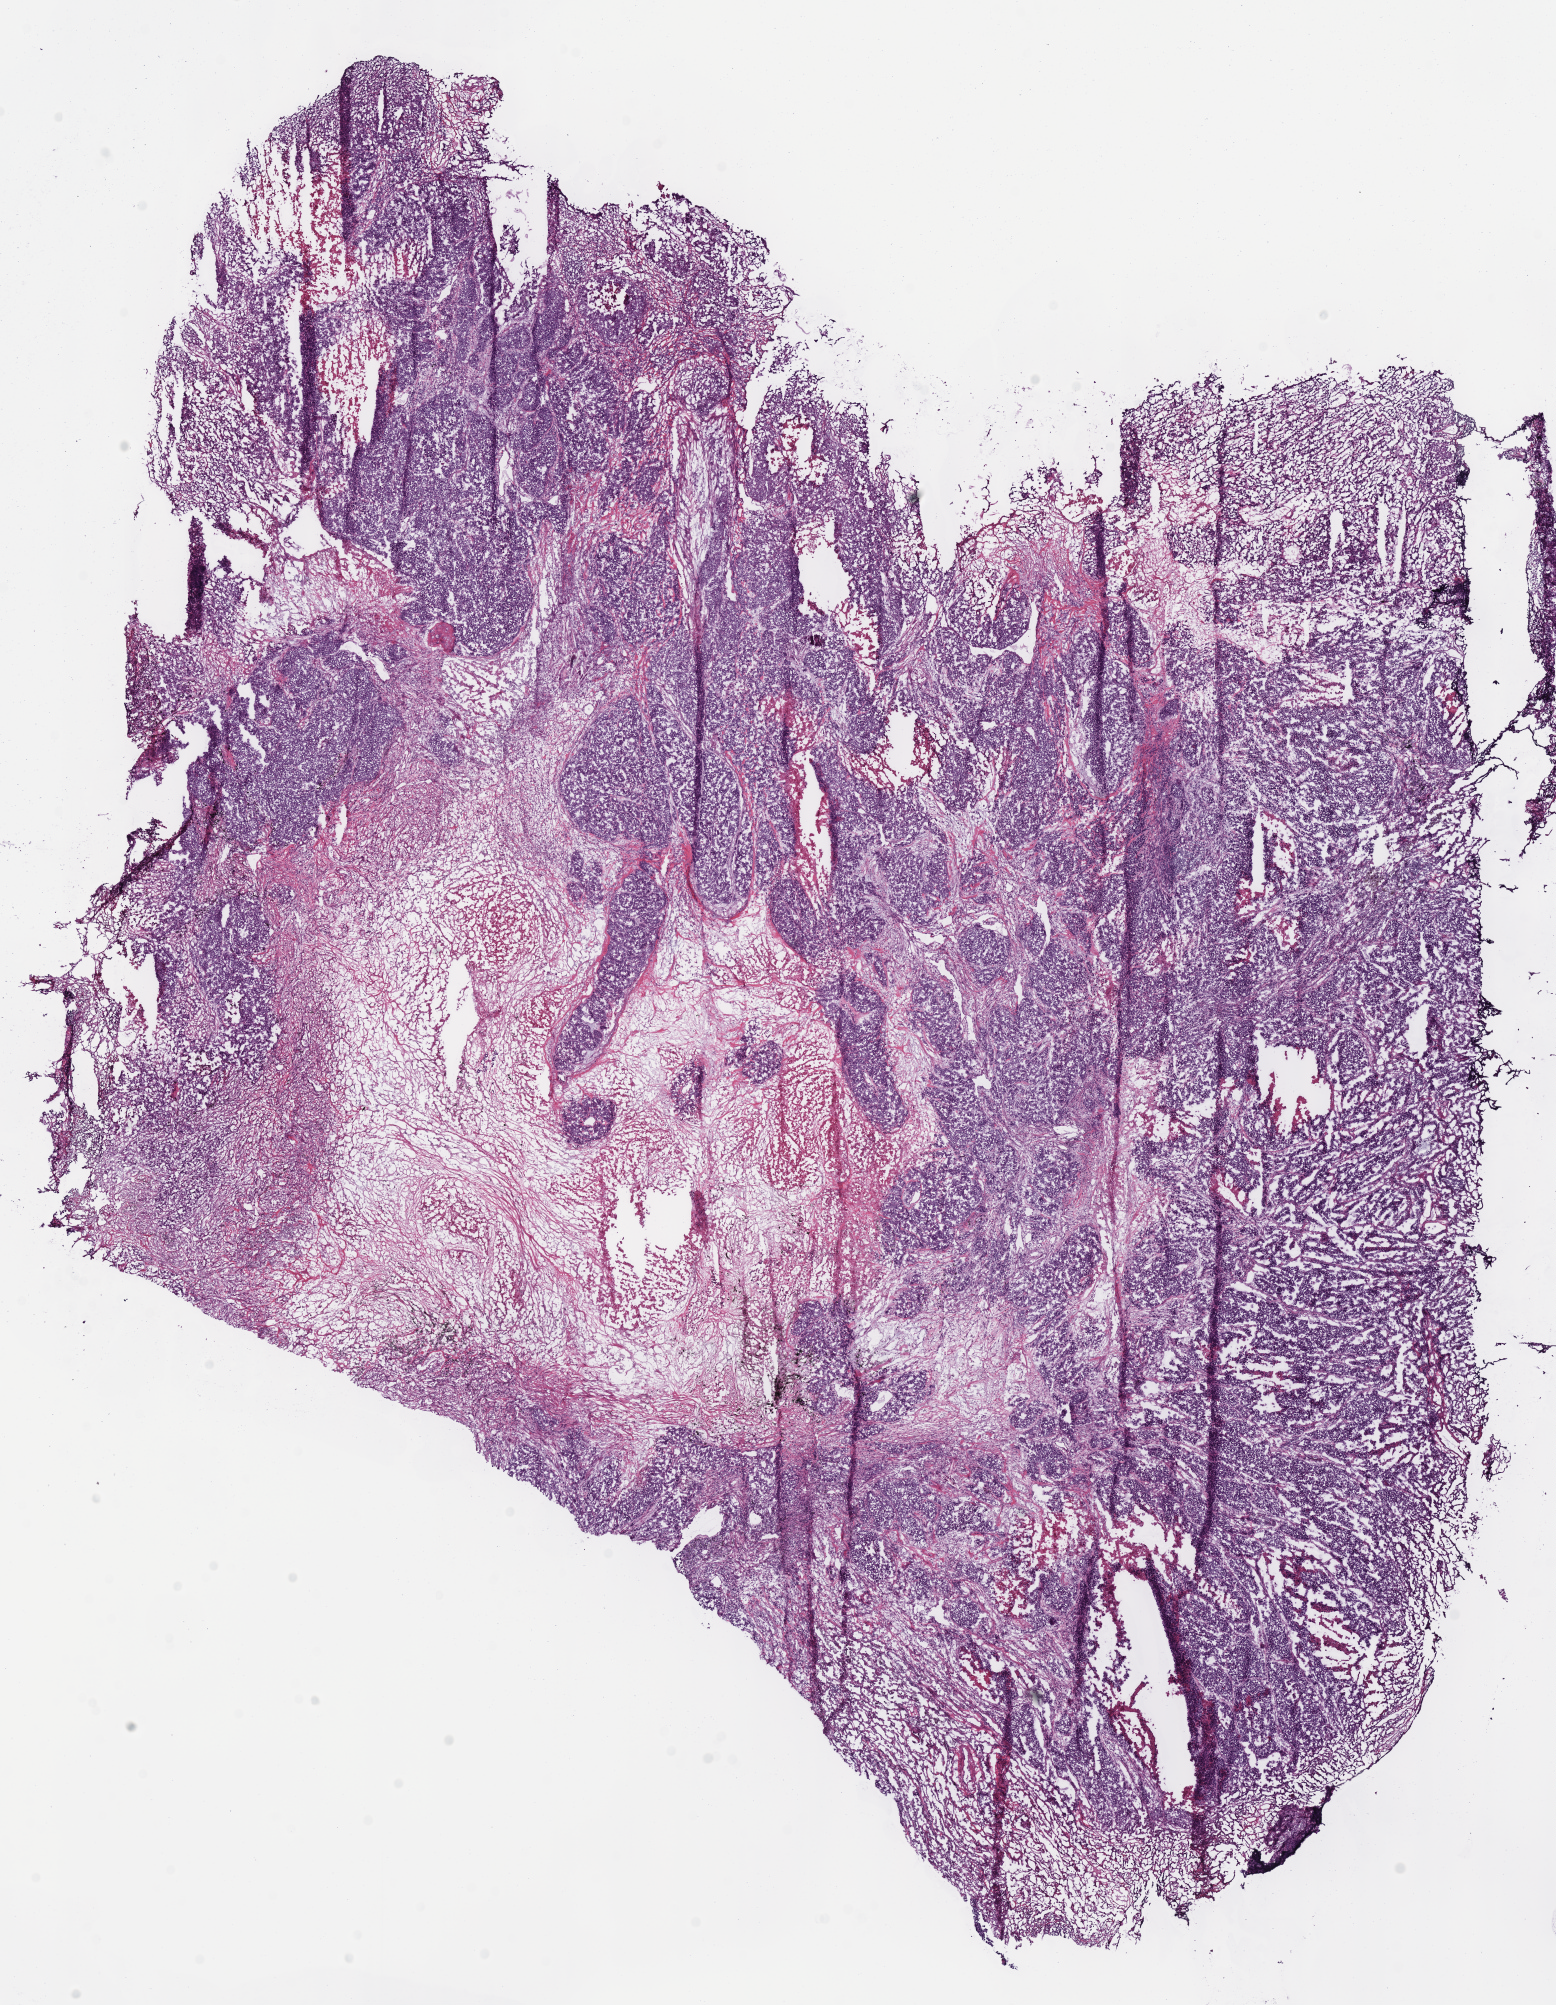
Digitized H&E tissue section (whole slide), a low-resolution overview of the entire scanned area, about 12.2 x 15.8 mm (slide scanned at 40x); frozen section; primary tumour sample from the lung. Male patient; age at initial diagnosis 44 years. Pathologist review of this section (percent, as recorded): tumour cells 75%, tumour nuclei 80%, normal cells 0%, stromal cells 10%, necrosis 15%.
- AJCC pathologic stage: IB
- diagnosis: Adenocarcinoma, NOS (upper lobe, lung)